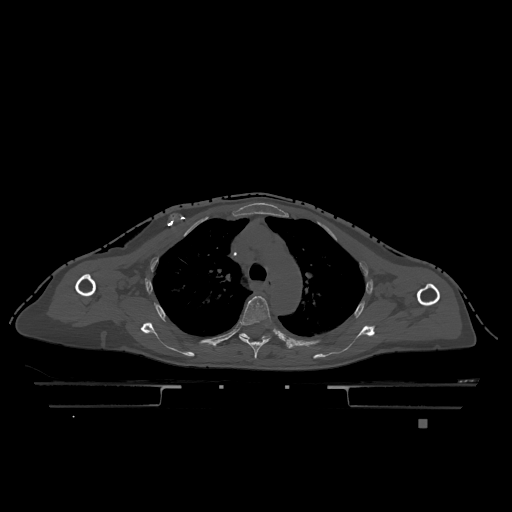
CT including the spine, one axial slice; slice 869 of 1317 in the series (ordered by position); bone window (W 1800 / L 400 HU); 0.5 mm slice thickness; 512 × 512 image matrix, field of view 500 × 500 mm. Patient: female, 74 years. Case-level facts recorded for this patient, not image findings: primary cancer: lung.
Outlined on this slice (semi-automatically segmented with operator editing):
- T4 vertebra: bounding box <239,296,271,359> (left, top, right, bottom; pixels)
- T5 vertebra: <239,333,269,339>